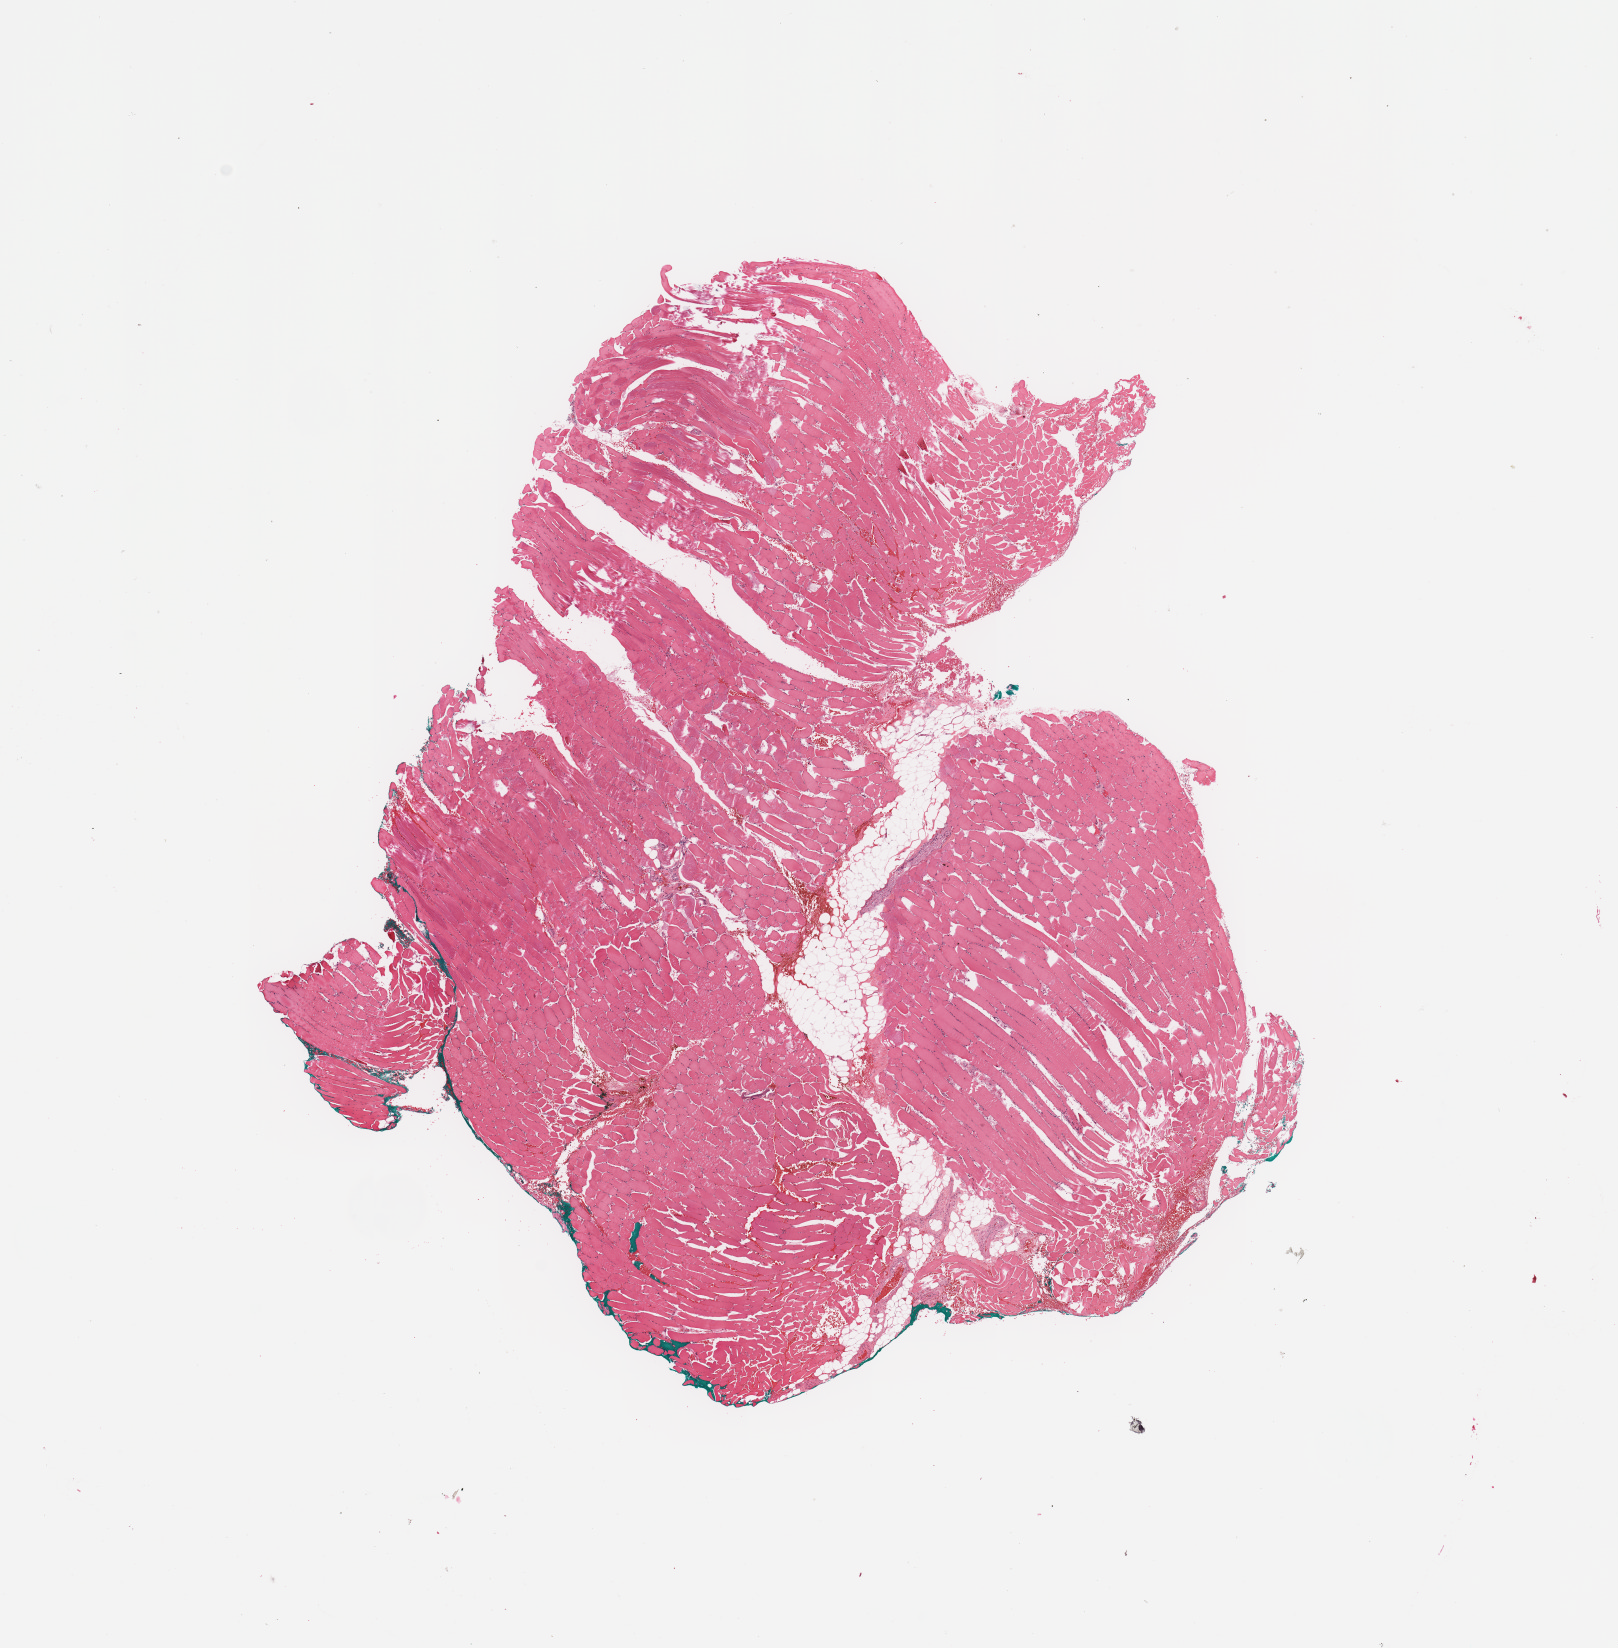
Digitized H&E-stained tissue section (whole slide), low-resolution overview of the scanned area, about 12.8 x 13.0 mm (from a 20x scan); normal (non-tumour) tissue sample. 60-year-old male patient.
This section: normal (non-tumour) tissue from the same patient. Patient diagnosis (cohort enrolment): sarcoma (site not recorded at cohort level).